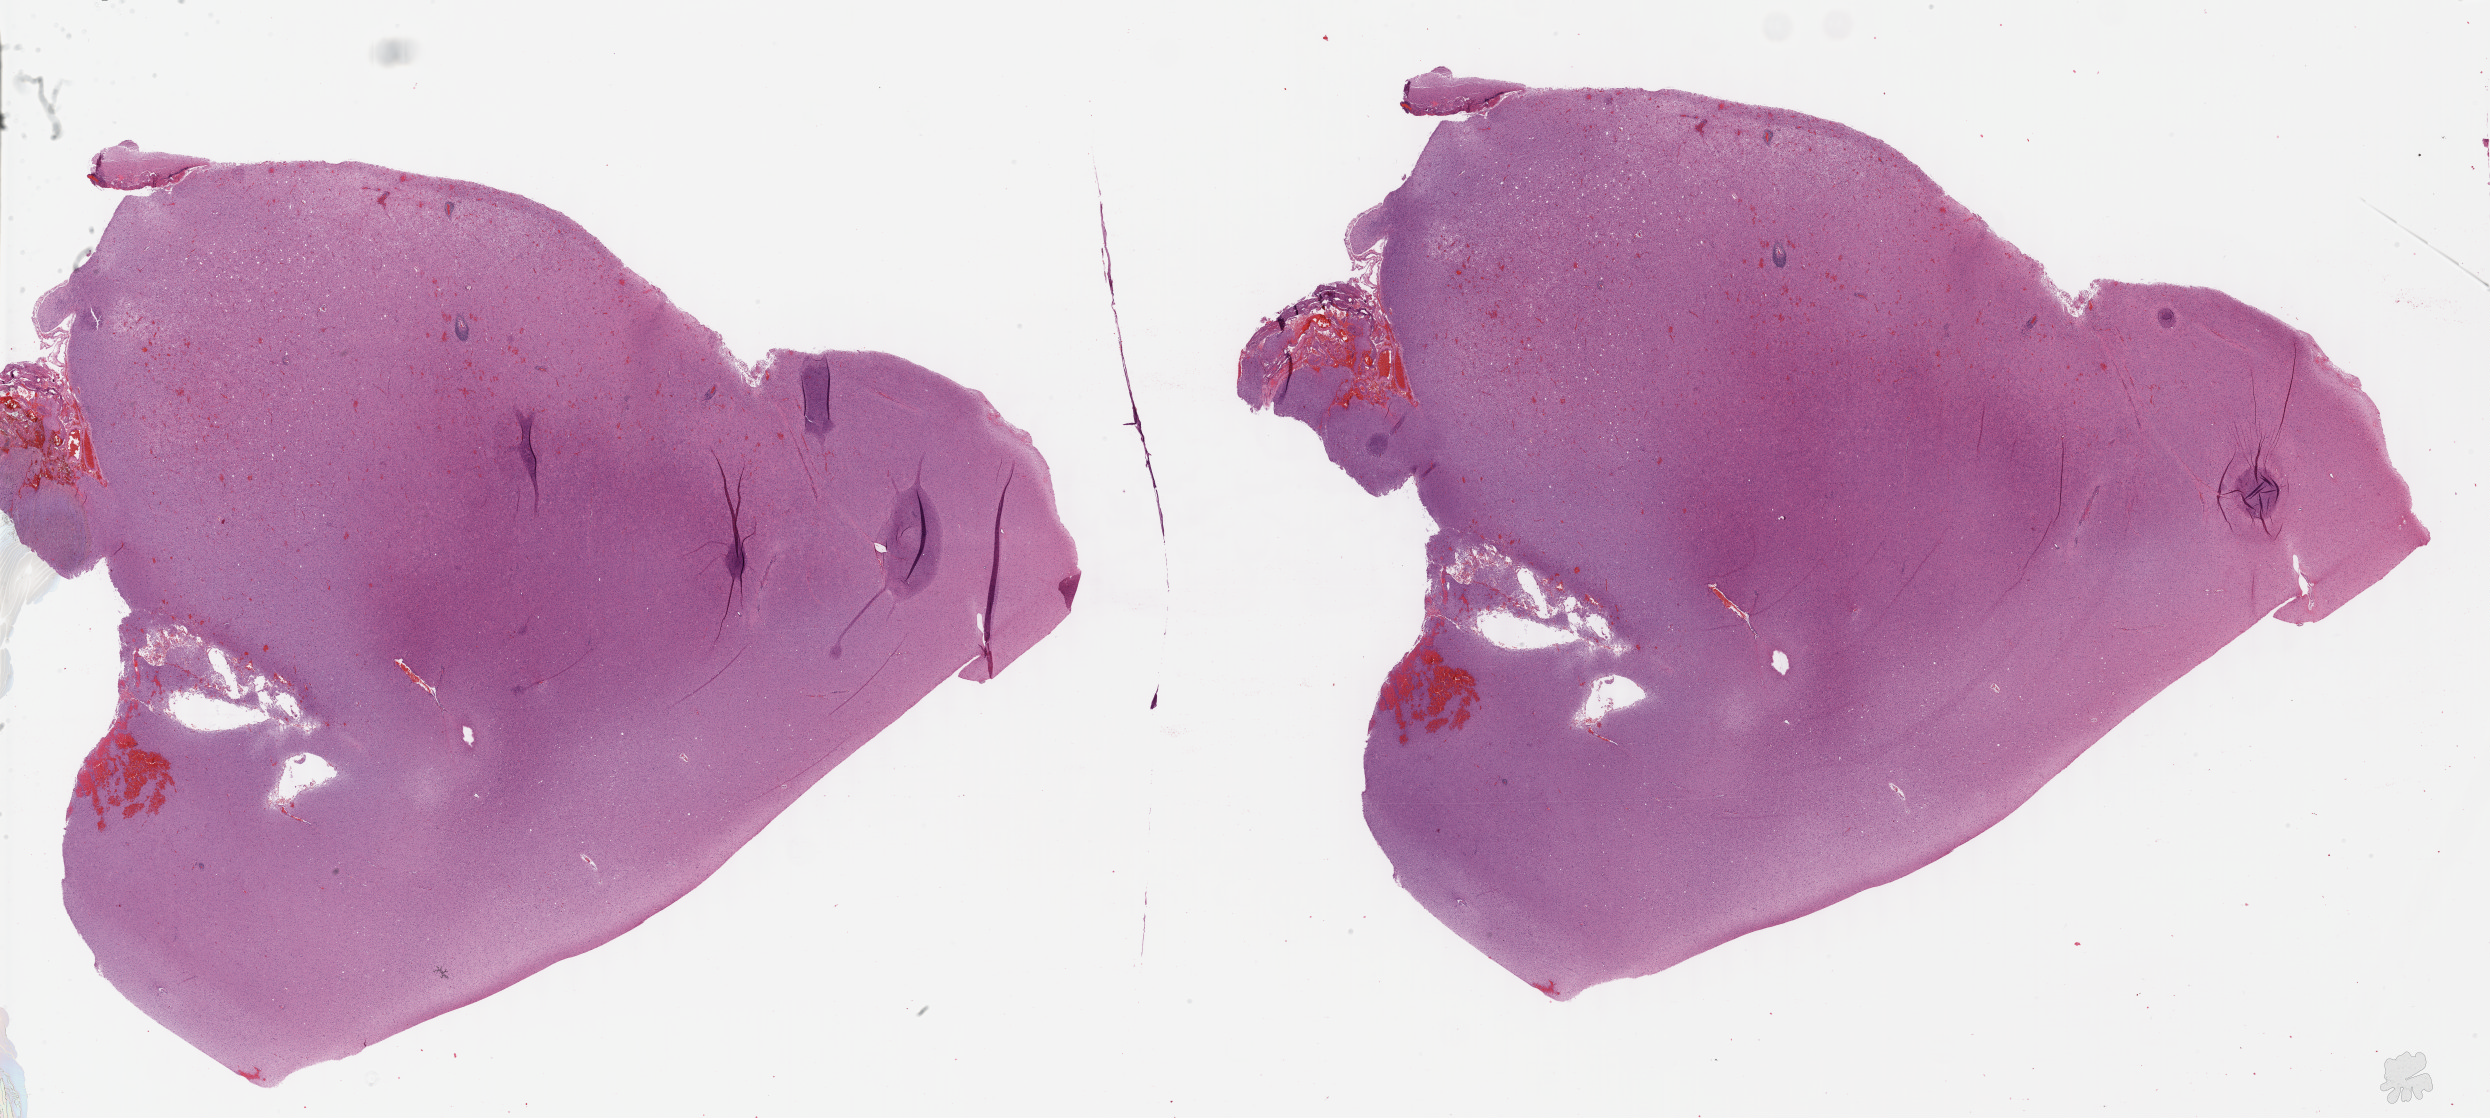
Whole-slide histology image, Hematoxylin and eosin (H&E) stained, a low-resolution overview of the entire scanned area, about 40.2 x 18.1 mm (slide scanned at 40x). Formalin-fixed paraffin-embedded (FFPE) diagnostic section. Sample: primary tumour, brain. Male patient; age at initial diagnosis 32 years. Histologic grade: G3 (poorly differentiated).
Pathologic diagnosis: Mixed glioma (cerebrum).